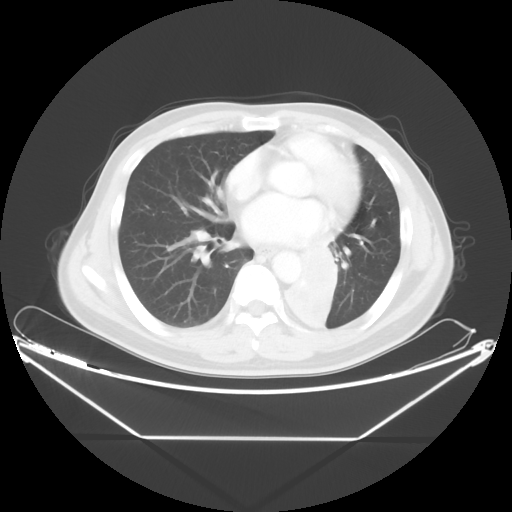
Chest CT, one axial slice; slice 21 of 48 in the series (ordered by position); 120 kVp; lung window (W 1500 / L -600 HU); 512 × 512 image matrix. Male patient, age 58 years. From the clinical record (not read from this slice): clinical TNM (as recorded): T3 N3 M0.
Structures marked on this image (rectangle marked by the reading radiologist):
- lung tumour (recorded histology: squamous cell carcinoma): bounding box (x1, y1, x2, y2) in pixels: (281, 243, 350, 339)